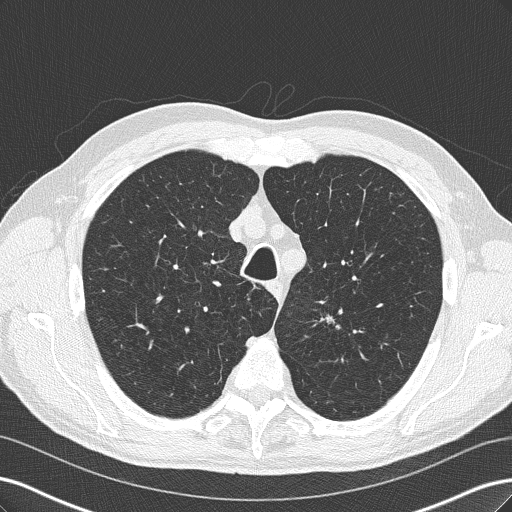
Low-dose screening chest CT, axial slice, third annual screen, lung window (W 1500 / L -600 HU), 2 mm slice thickness, lung (sharp) reconstruction kernel (B50f), slice 46 of 219 in the series. Male participant, aged 66 years at enrolment. Current smoker at enrolment.
Expert-annotated lung lesion, bounding box [x1, y1, x2, y2] px = [301, 300, 352, 347]. Screening reader's record for this exam (one nodule recorded; not confirmed to be the boxed lesion): non-calcified nodule or mass ≥4 mm, left upper lobe, 14 × 9 mm, spiculated (stellate) margins, soft tissue attenuation, pre-existing on the prior screen: yes; interval growth: yes. Participant outcome: lung cancer diagnosed 19 days after this screen — squamous cell carcinoma, NOS, left upper lobe, poorly differentiated (G3), stage IA (AJCC 6th edition), 15 mm at pathology.